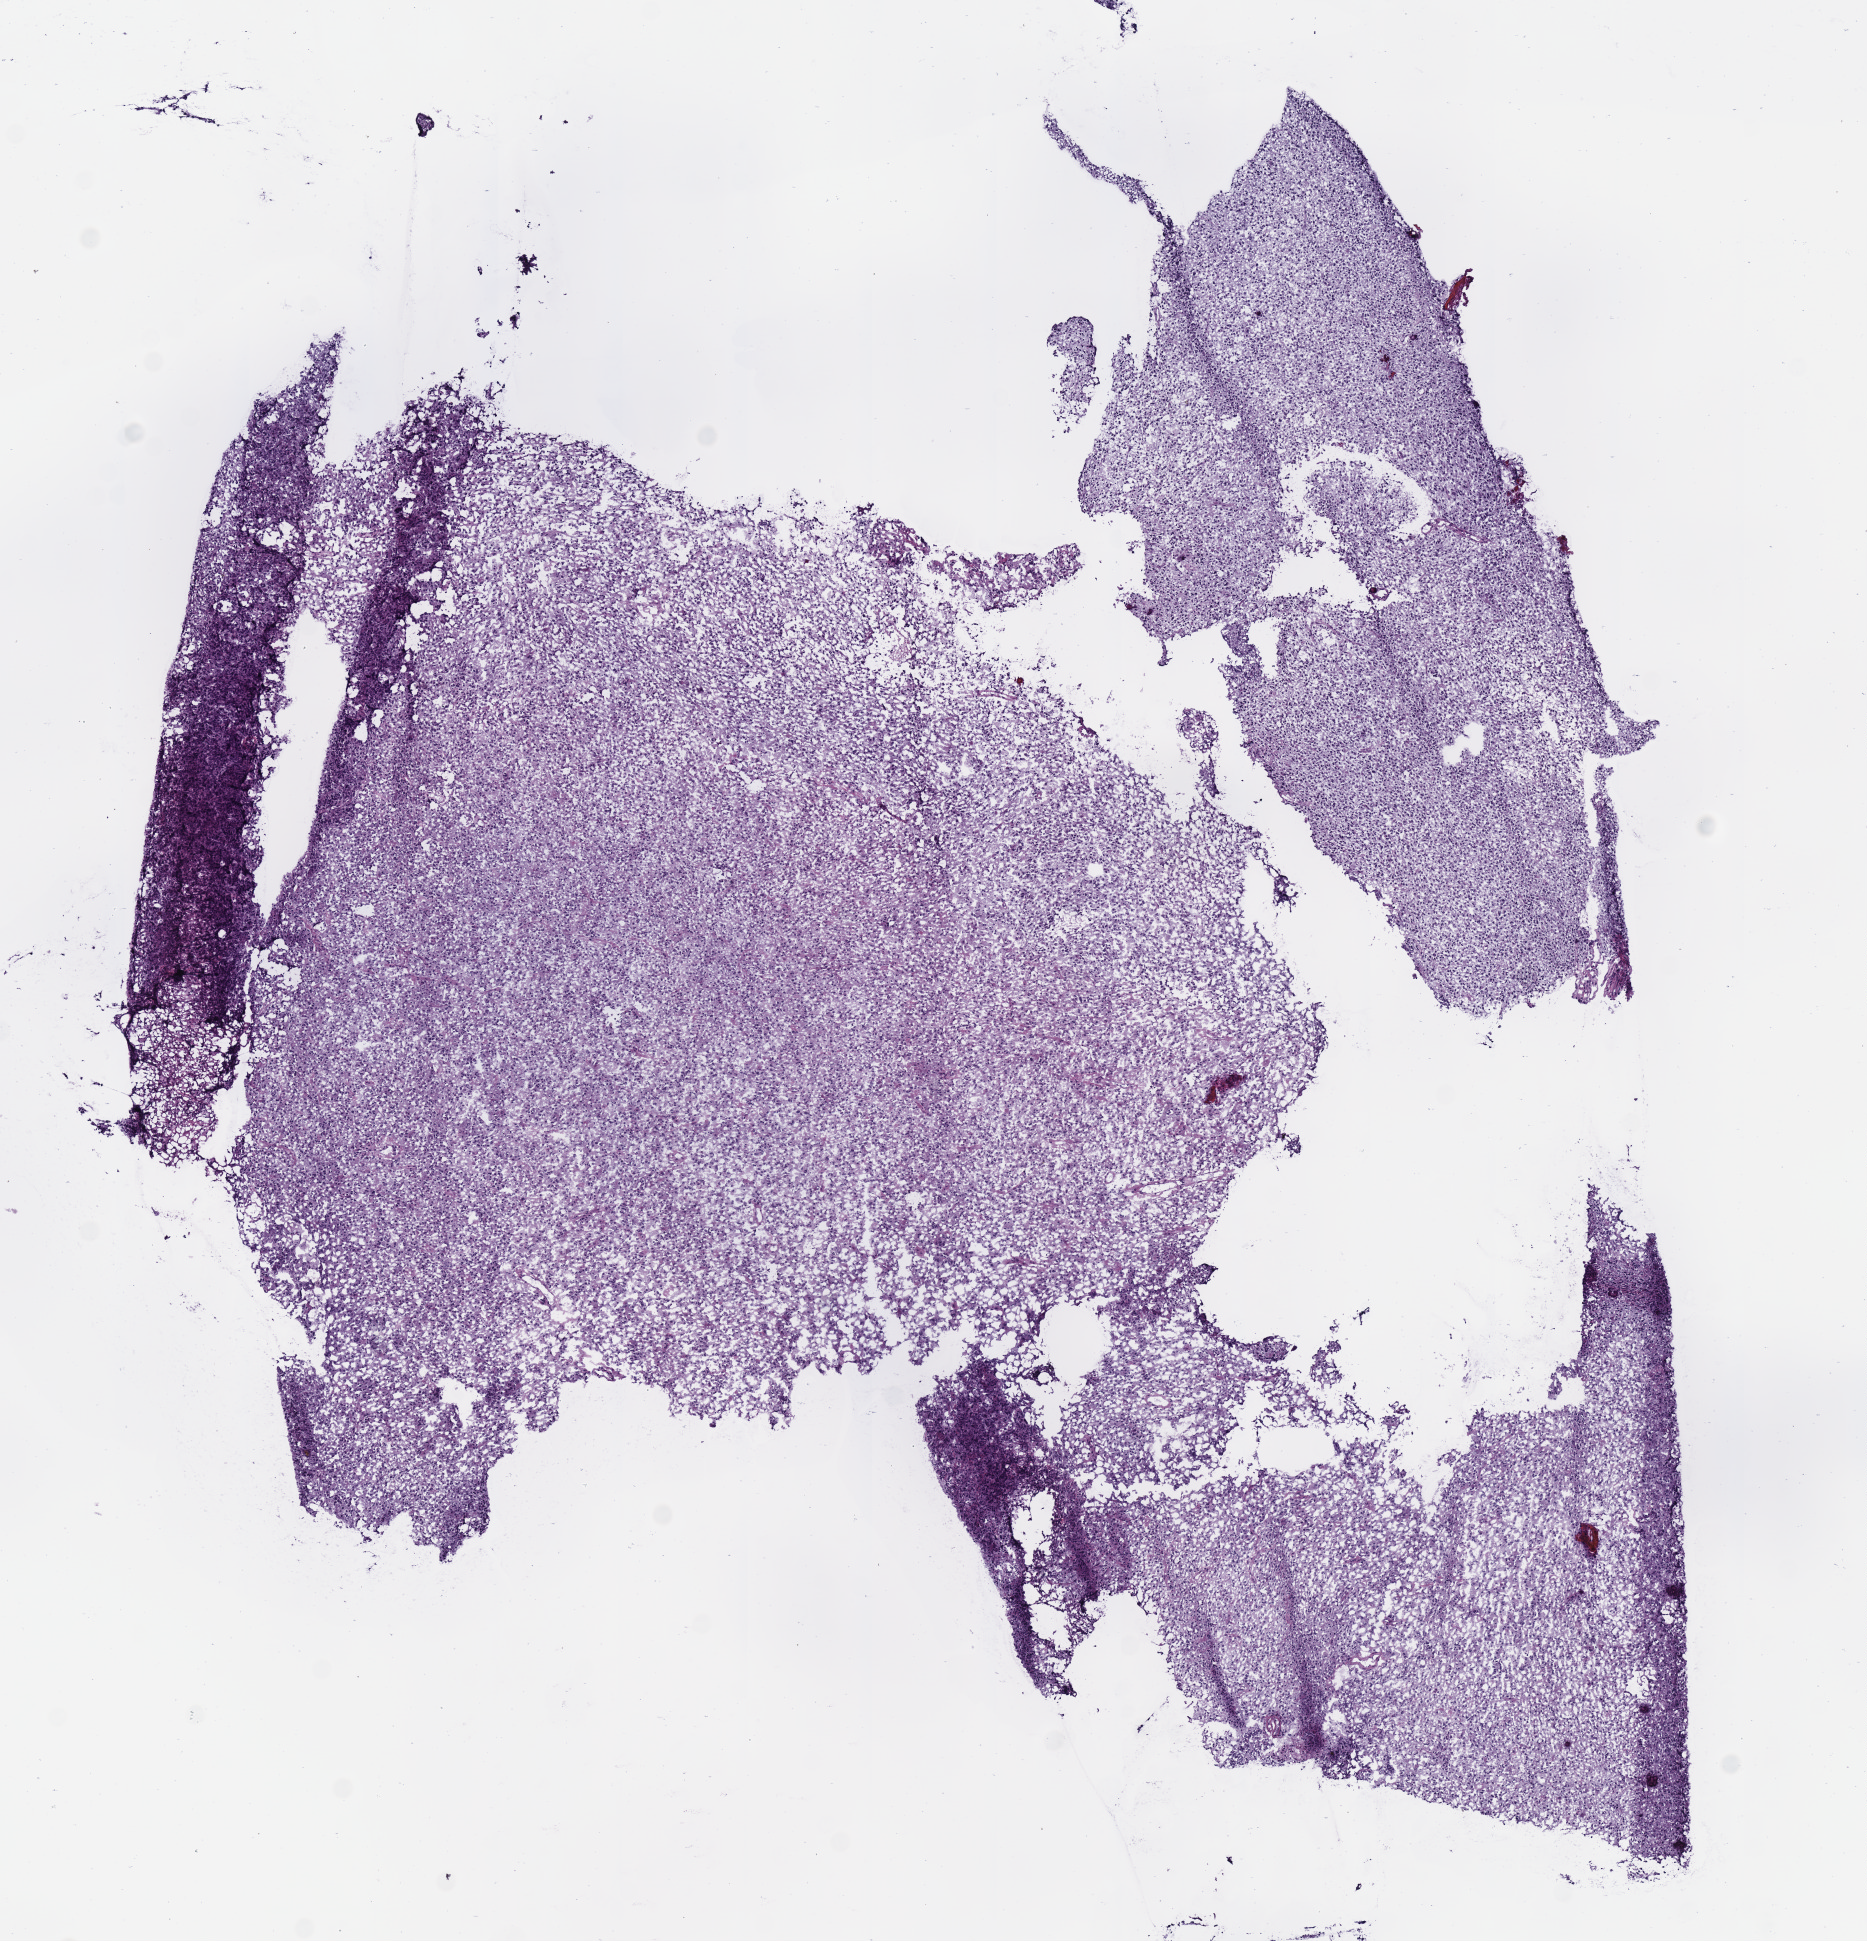
Digitized Hematoxylin and eosin (H&E) stained tissue section (whole slide) — low-resolution overview of the scanned area, about 7.3 x 7.6 mm, frozen section from the bottom of the tissue portion, sample: primary tumour, brain. Female, age 30 years at initial diagnosis. Histologic grade: G2 (moderately differentiated). Slide review estimates, as recorded: tumour cells 100%, tumour nuclei 80%, normal cells 0%, stromal cells 0%, necrosis 0%.
* histologic diagnosis: Oligodendroglioma, NOS (cerebrum)